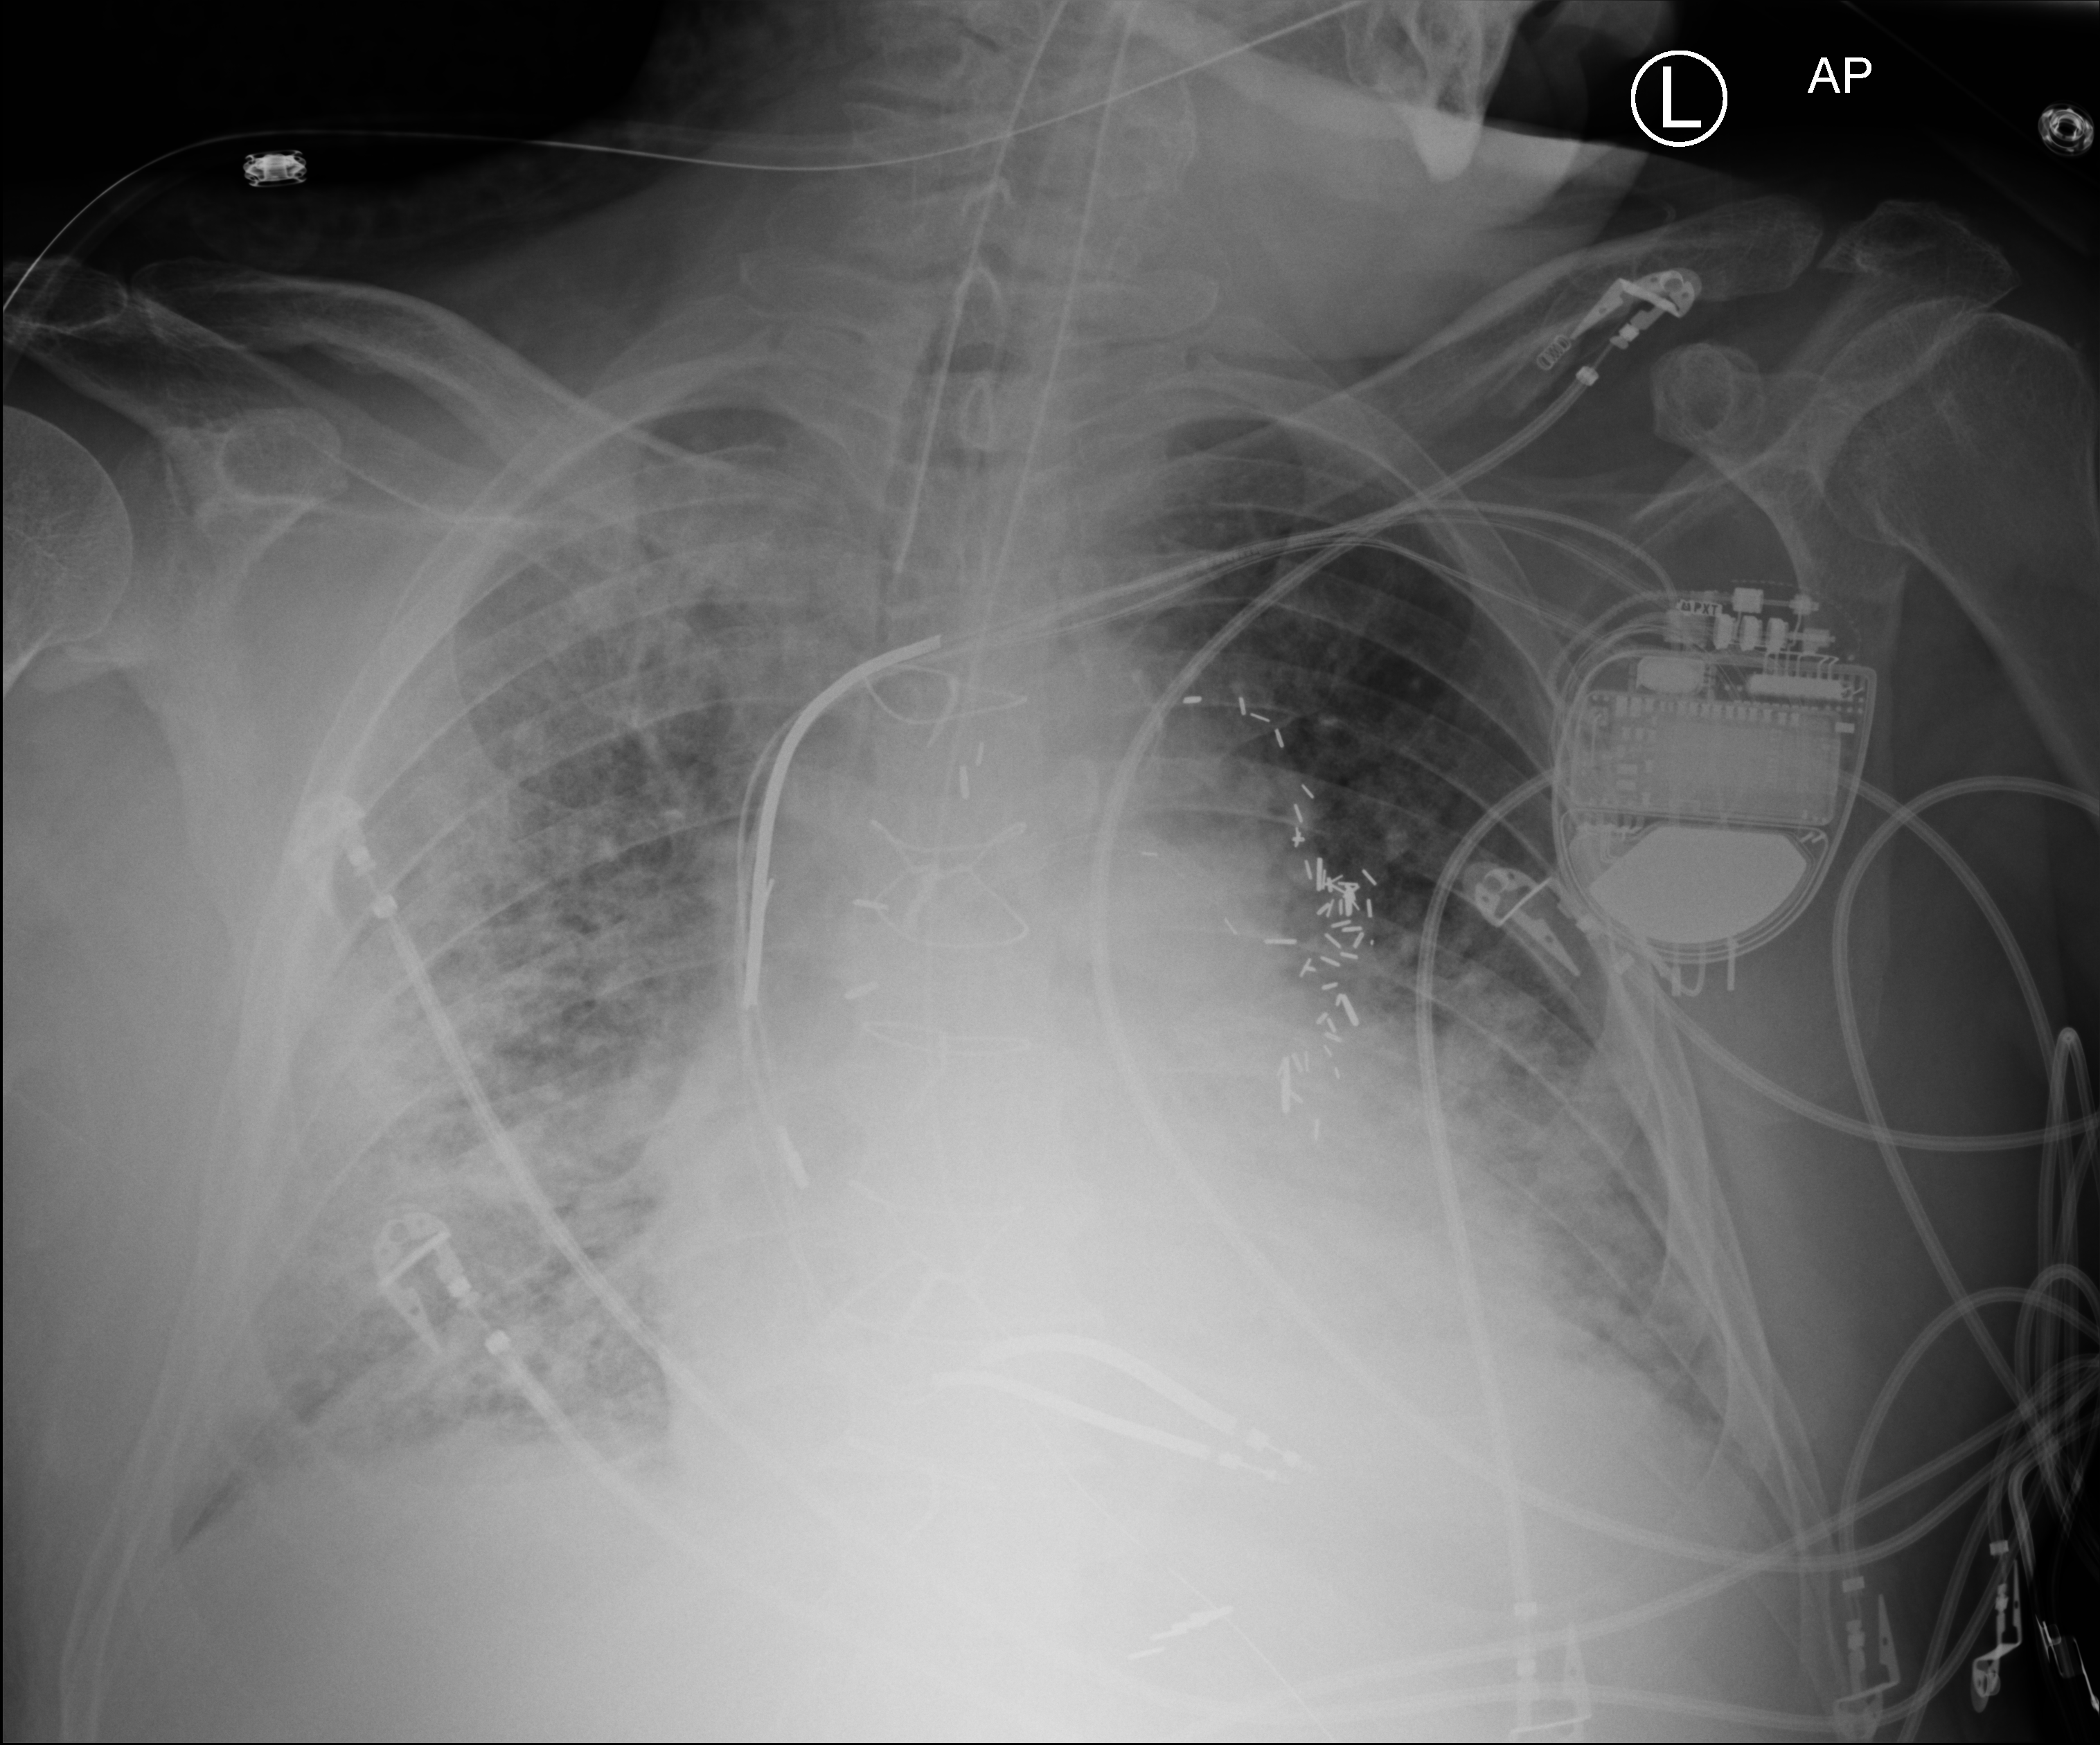
Portable chest radiograph, anteroposterior (AP) projection. Male patient hospitalised with COVID-19, age 60–74 years.
Hospital-stay facts (about this admission, not read from this image; timing relative to this image not recorded):
- mechanically ventilated during this hospital stay: yes
- admitted to intensive care during this hospital stay: yes
- smoking status (admission record): never